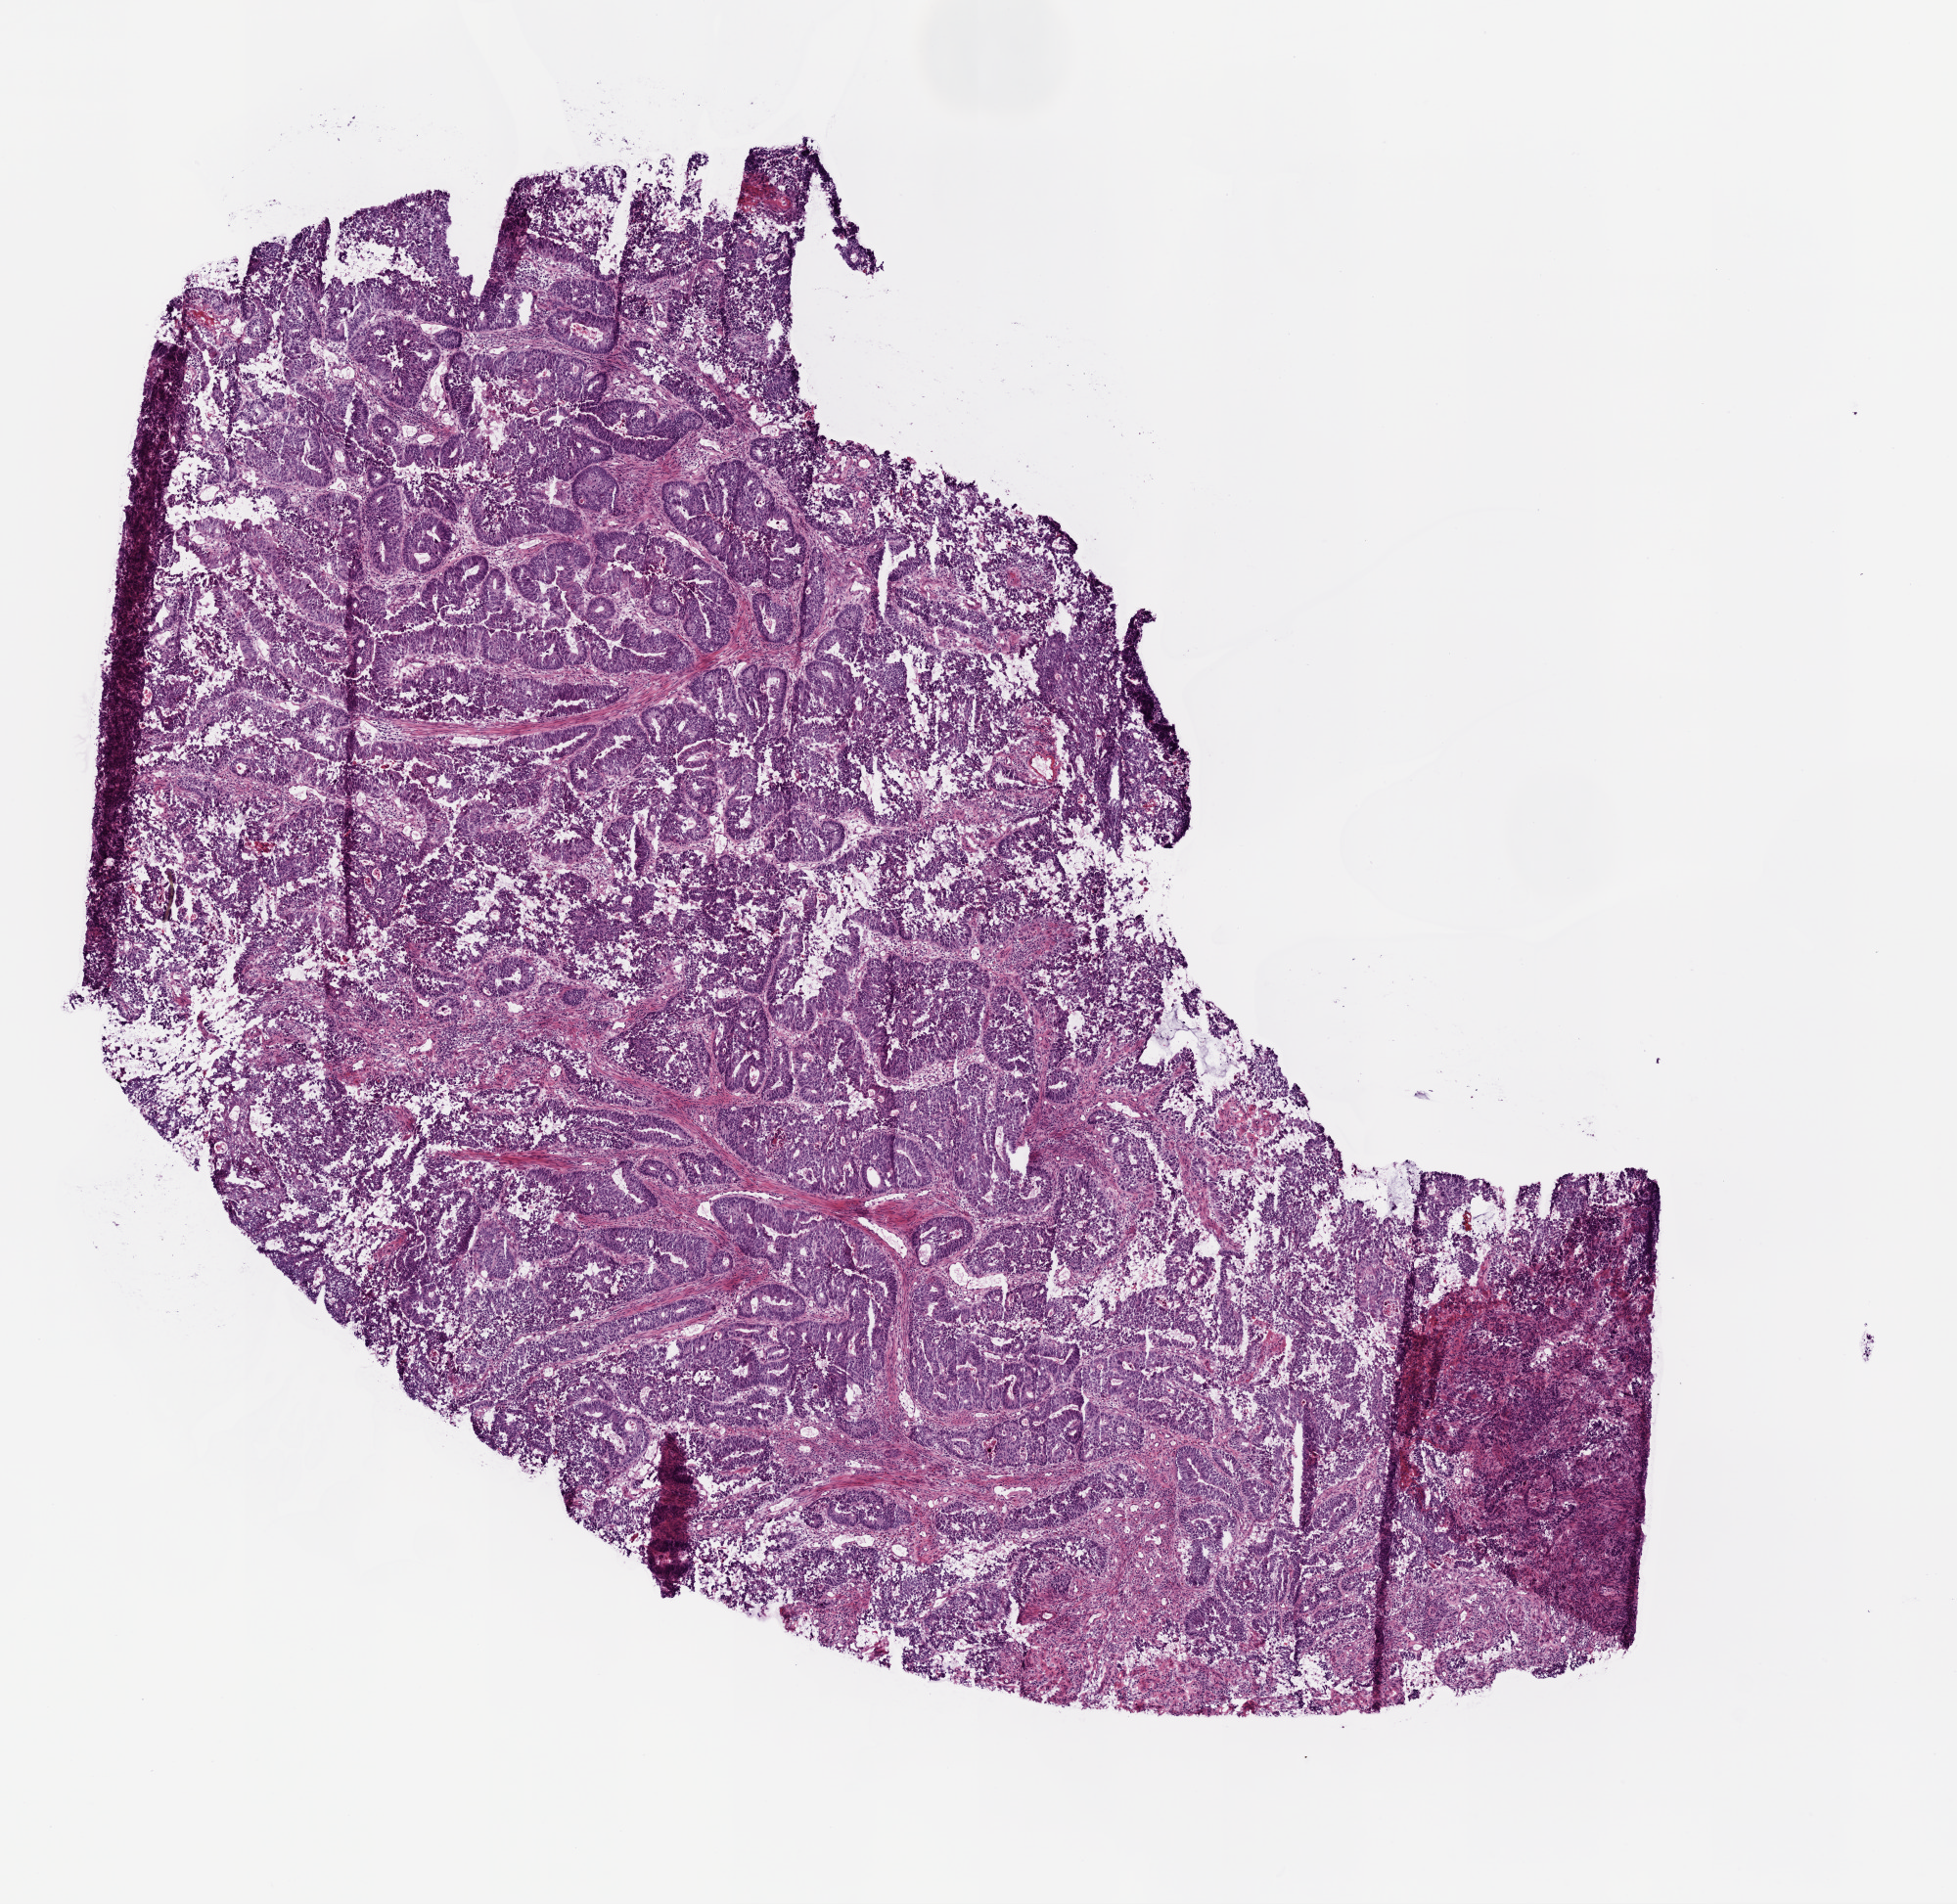
Digitized H&E tissue section (whole slide), whole scanned area (about 8.0 x 7.8 mm) shown as a low-resolution overview, frozen section from the top of the tissue portion, sample: primary tumour, colon. Patient: female, age at initial diagnosis 55 years. Pathologist review of this section (percent, as recorded): tumour cells 100%, tumour nuclei 90%, normal cells 0%, stromal cells 0%, necrosis 0%.
Histologic diagnosis: Adenocarcinoma, NOS (sigmoid colon). AJCC pathologic stage: I (6th edition). Lymph nodes positive (case pathology): 0 of 19 examined.